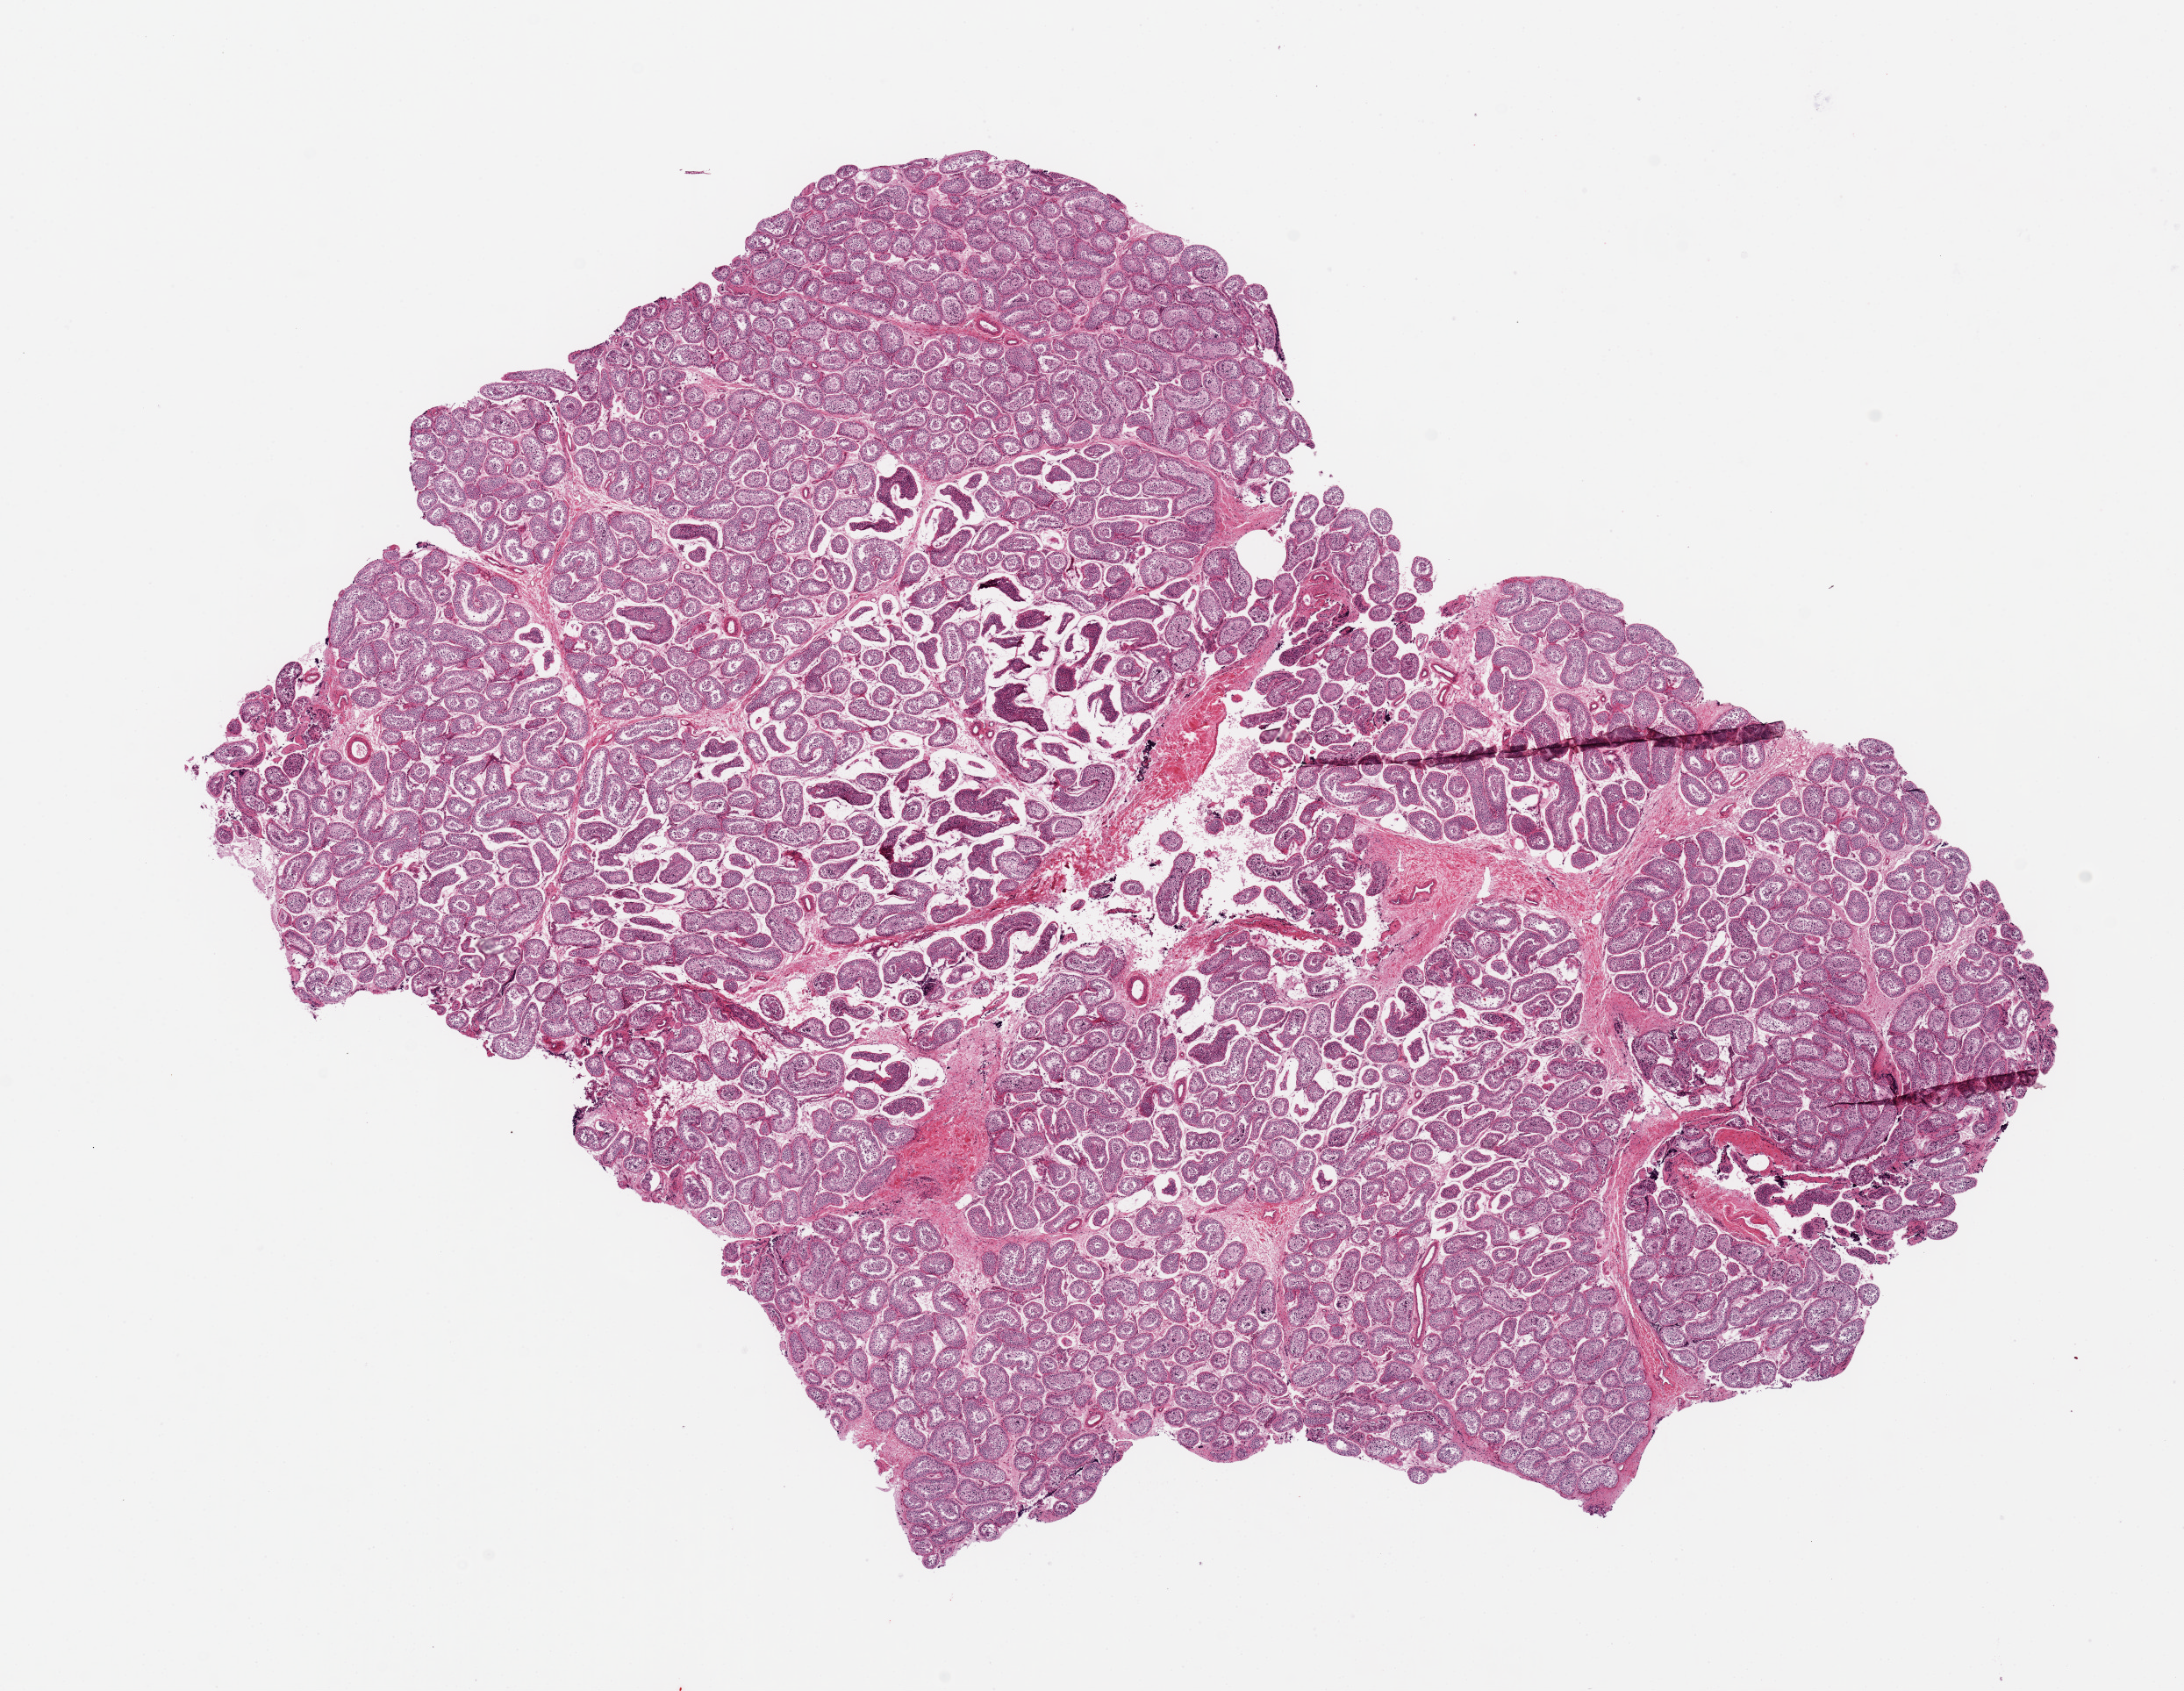
Hematoxylin and eosin (H&E) whole-slide image, brightfield, shown as a low-resolution overview of the whole scanned area (about 19.7 x 15.2 mm, from a 20x scan); PAXgene-fixed paraffin-embedded (PFPE) section; target tissue: testis; tissue donor sample. Male donor.
Pathologist's review note for this sample: 1 piece ~13x10mm. Spermatogenesis is present/within normal limits.